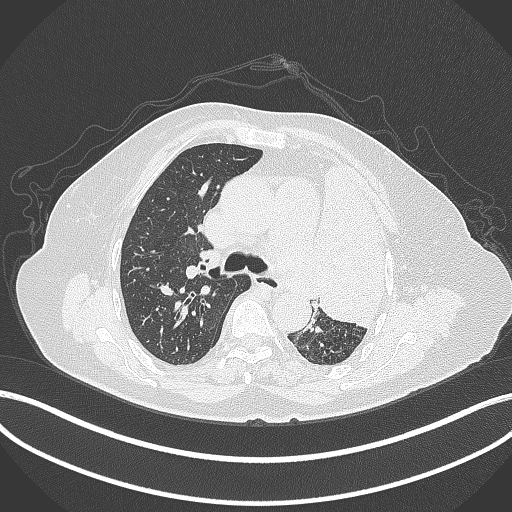
Chest CT, one axial slice. Position 254 of 399 along the scan axis. Reconstruction kernel B70f. Lung window (W 1500 / L -600 HU). 1 mm slice thickness. 512 × 512 image matrix. Female patient, age 75 years. From the clinical record (not read from this slice): clinical TNM (as recorded): T3 N3 M1.
Annotated regions visible in this slice (bounding box drawn by a radiologist):
- lung tumour (recorded histology: adenocarcinoma): bounding box <316,154,391,330> (left, top, right, bottom; pixels)